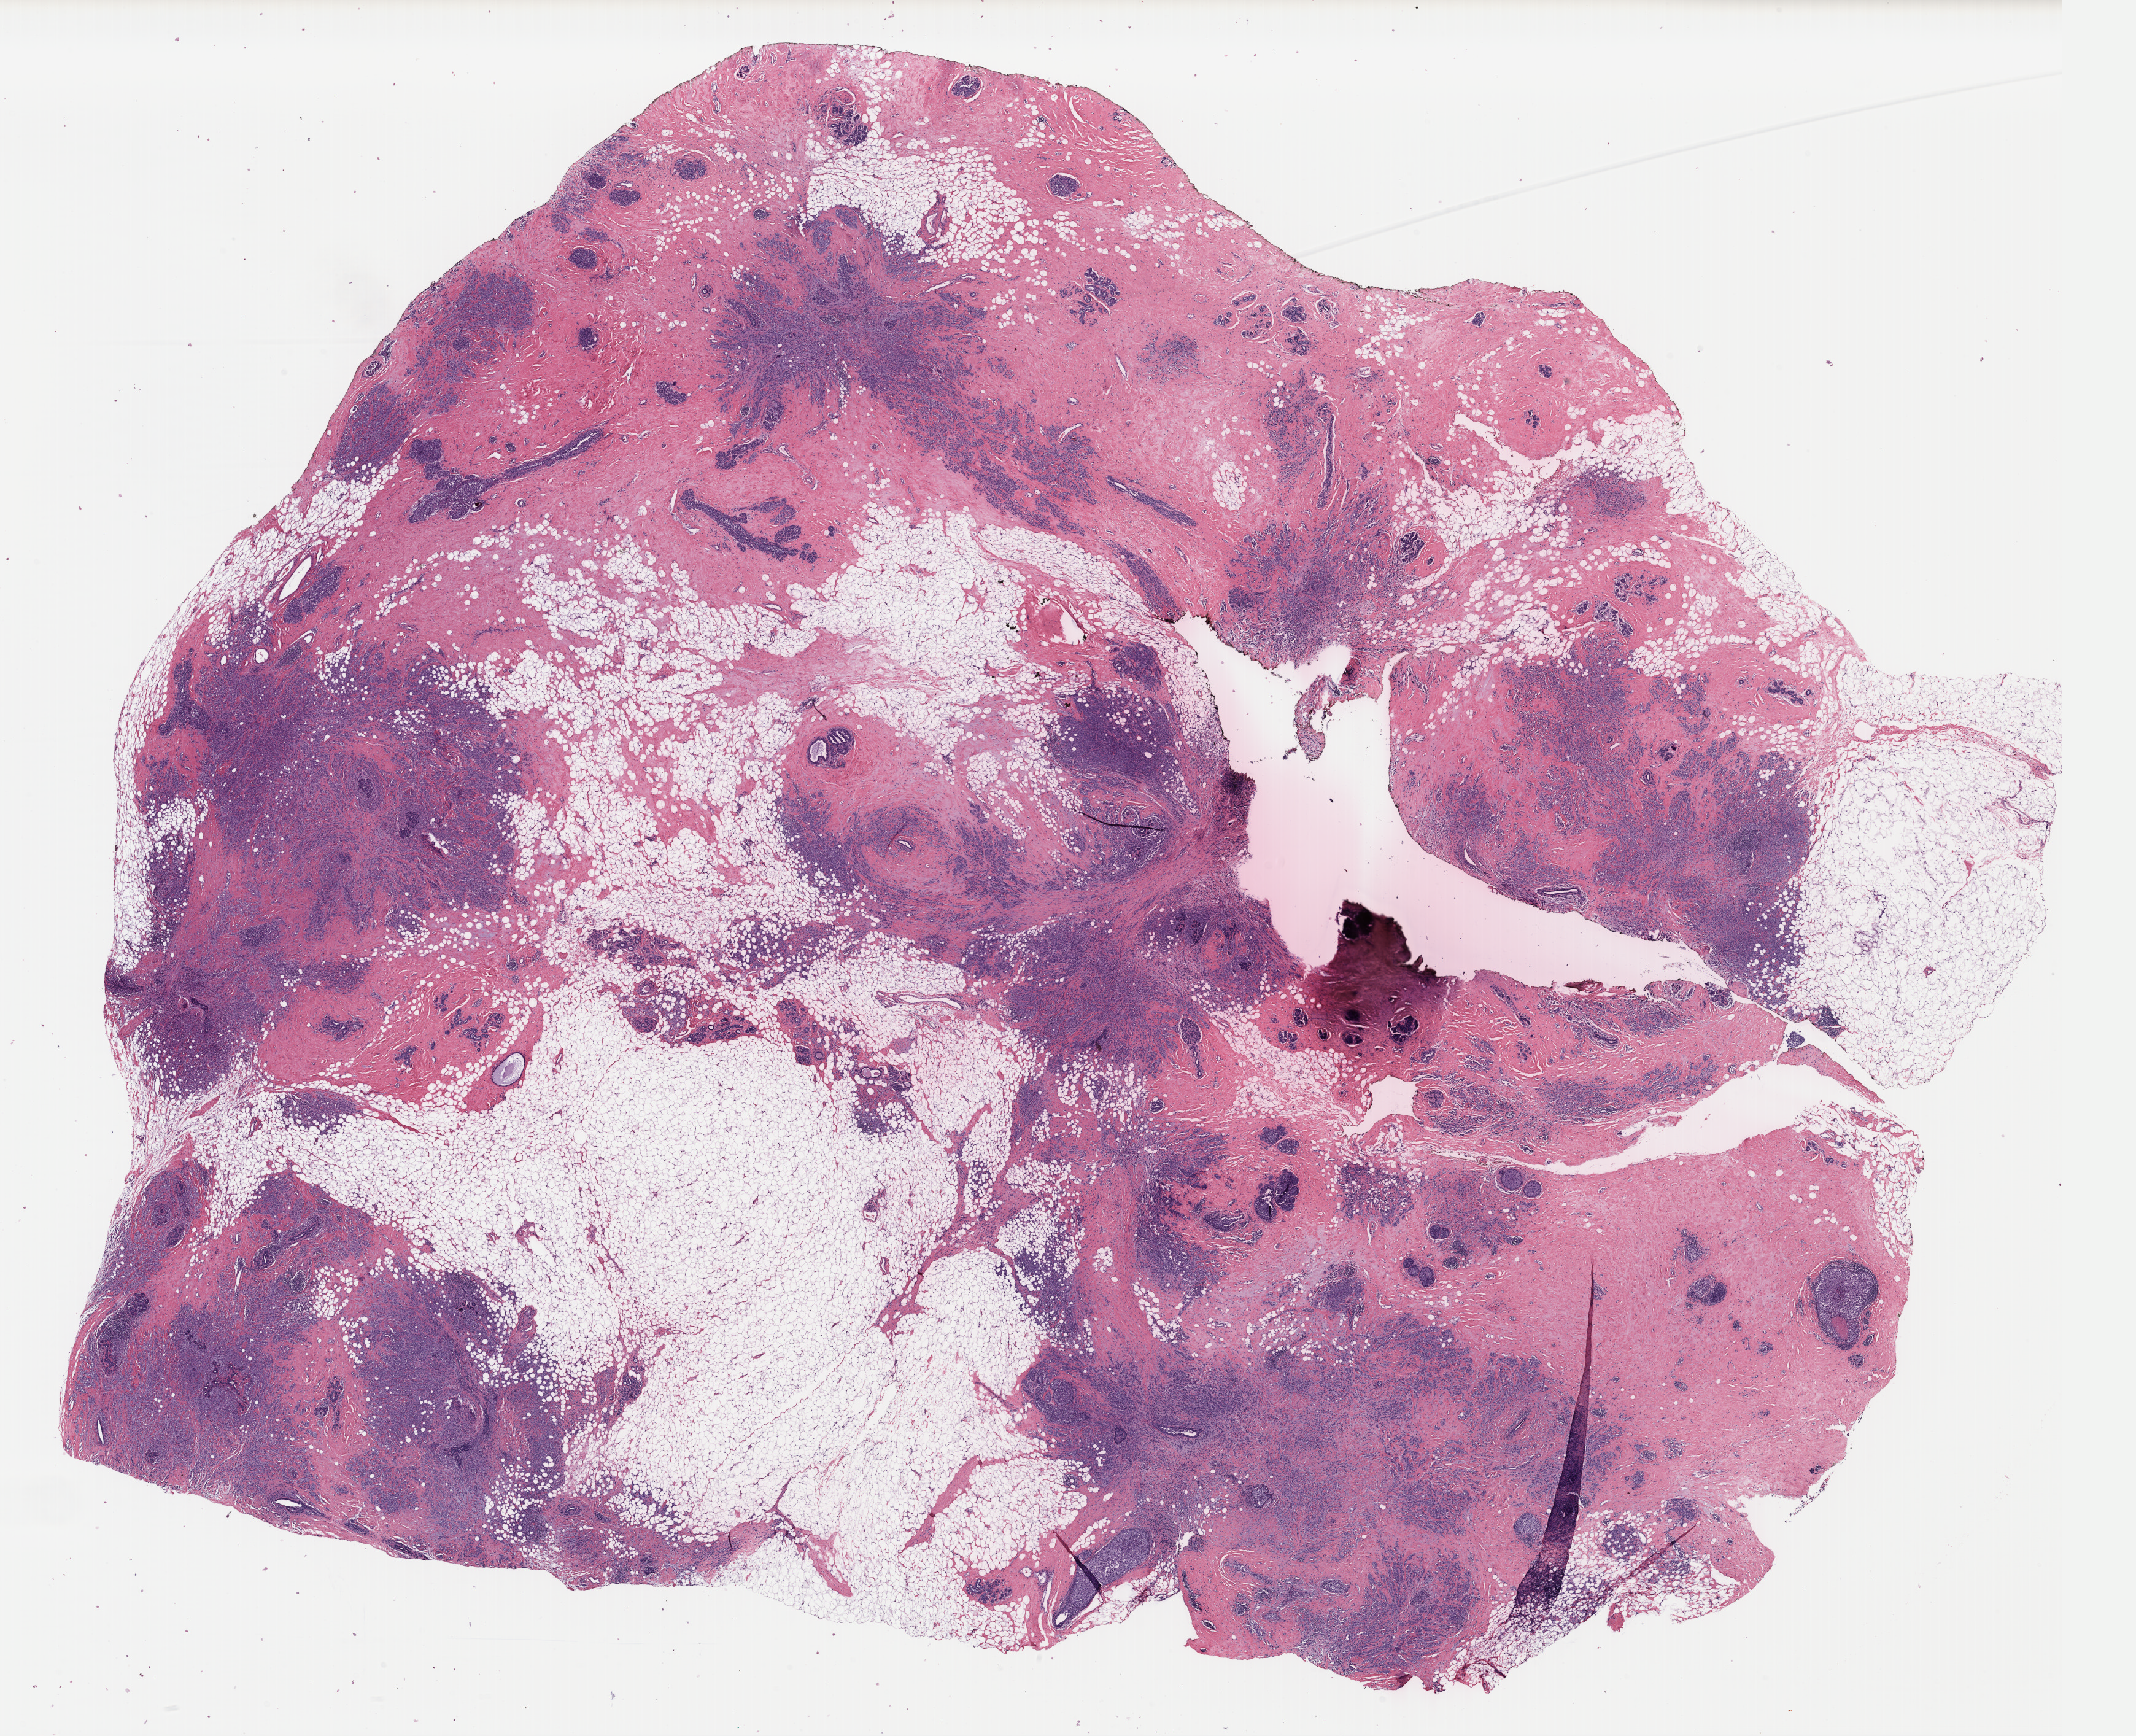
Digitized Hematoxylin and eosin (H&E) stained tissue section (whole slide) — shown as a low-resolution overview of the whole scanned area (about 27.4 x 22.2 mm, from a 40x scan); formalin-fixed paraffin-embedded (FFPE) diagnostic section; breast, primary tumour sample. Female, age 49 years at initial diagnosis.
TNM: T2 N3a M0. Lymph nodes positive (case pathology): 27 of 27 examined. AJCC pathologic stage: IIIC (7th edition). Histologic diagnosis: Lobular carcinoma, NOS.